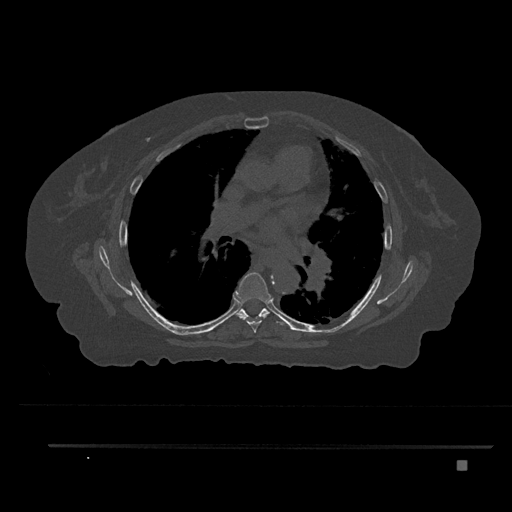
CT including the spine, one axial slice; slice 511 of 797 in the series (ordered by position); 120 kVp; bone window (W 1800 / L 400 HU); 0.5 mm slice thickness; 512 × 512 image matrix, field of view 437 × 437 mm. Patient: female, 76 years. From the clinical record (not read from this slice): primary cancer: lung; vertebrae with lytic lesions (as recorded): T11, L3.
Annotated regions visible in this slice (semi-automatic segmentation, software-assisted and operator-edited):
- T6 vertebra: box from (x=233, y=272) to (x=271, y=333) px
- T7 vertebra: (x=238, y=309)–(x=284, y=325)